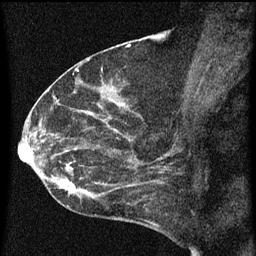
Breast MRI (dynamic contrast-enhanced), one sagittal slice. Slice 35 of 60 in the series (ordered by position). Dynamic contrast-enhanced series, image 2 of 3 at this slice position (ordered by acquisition). 1.5 T. TE 4.2 ms, TR 8 ms. 256 × 256 image matrix. Female patient, age 54 years.
Outlined on this slice (semi-automatic segmentation, software-assisted and operator-edited):
- analysis volume of interest (the breast-tissue region the enhancement analysis was run in; not a lesion): bounding box (x1, y1, x2, y2) in pixels: (49, 138, 164, 209)
- tumour enhancement mask (voxels above the 70 % enhancement threshold inside the analysis volume of interest): (58, 138, 164, 207)